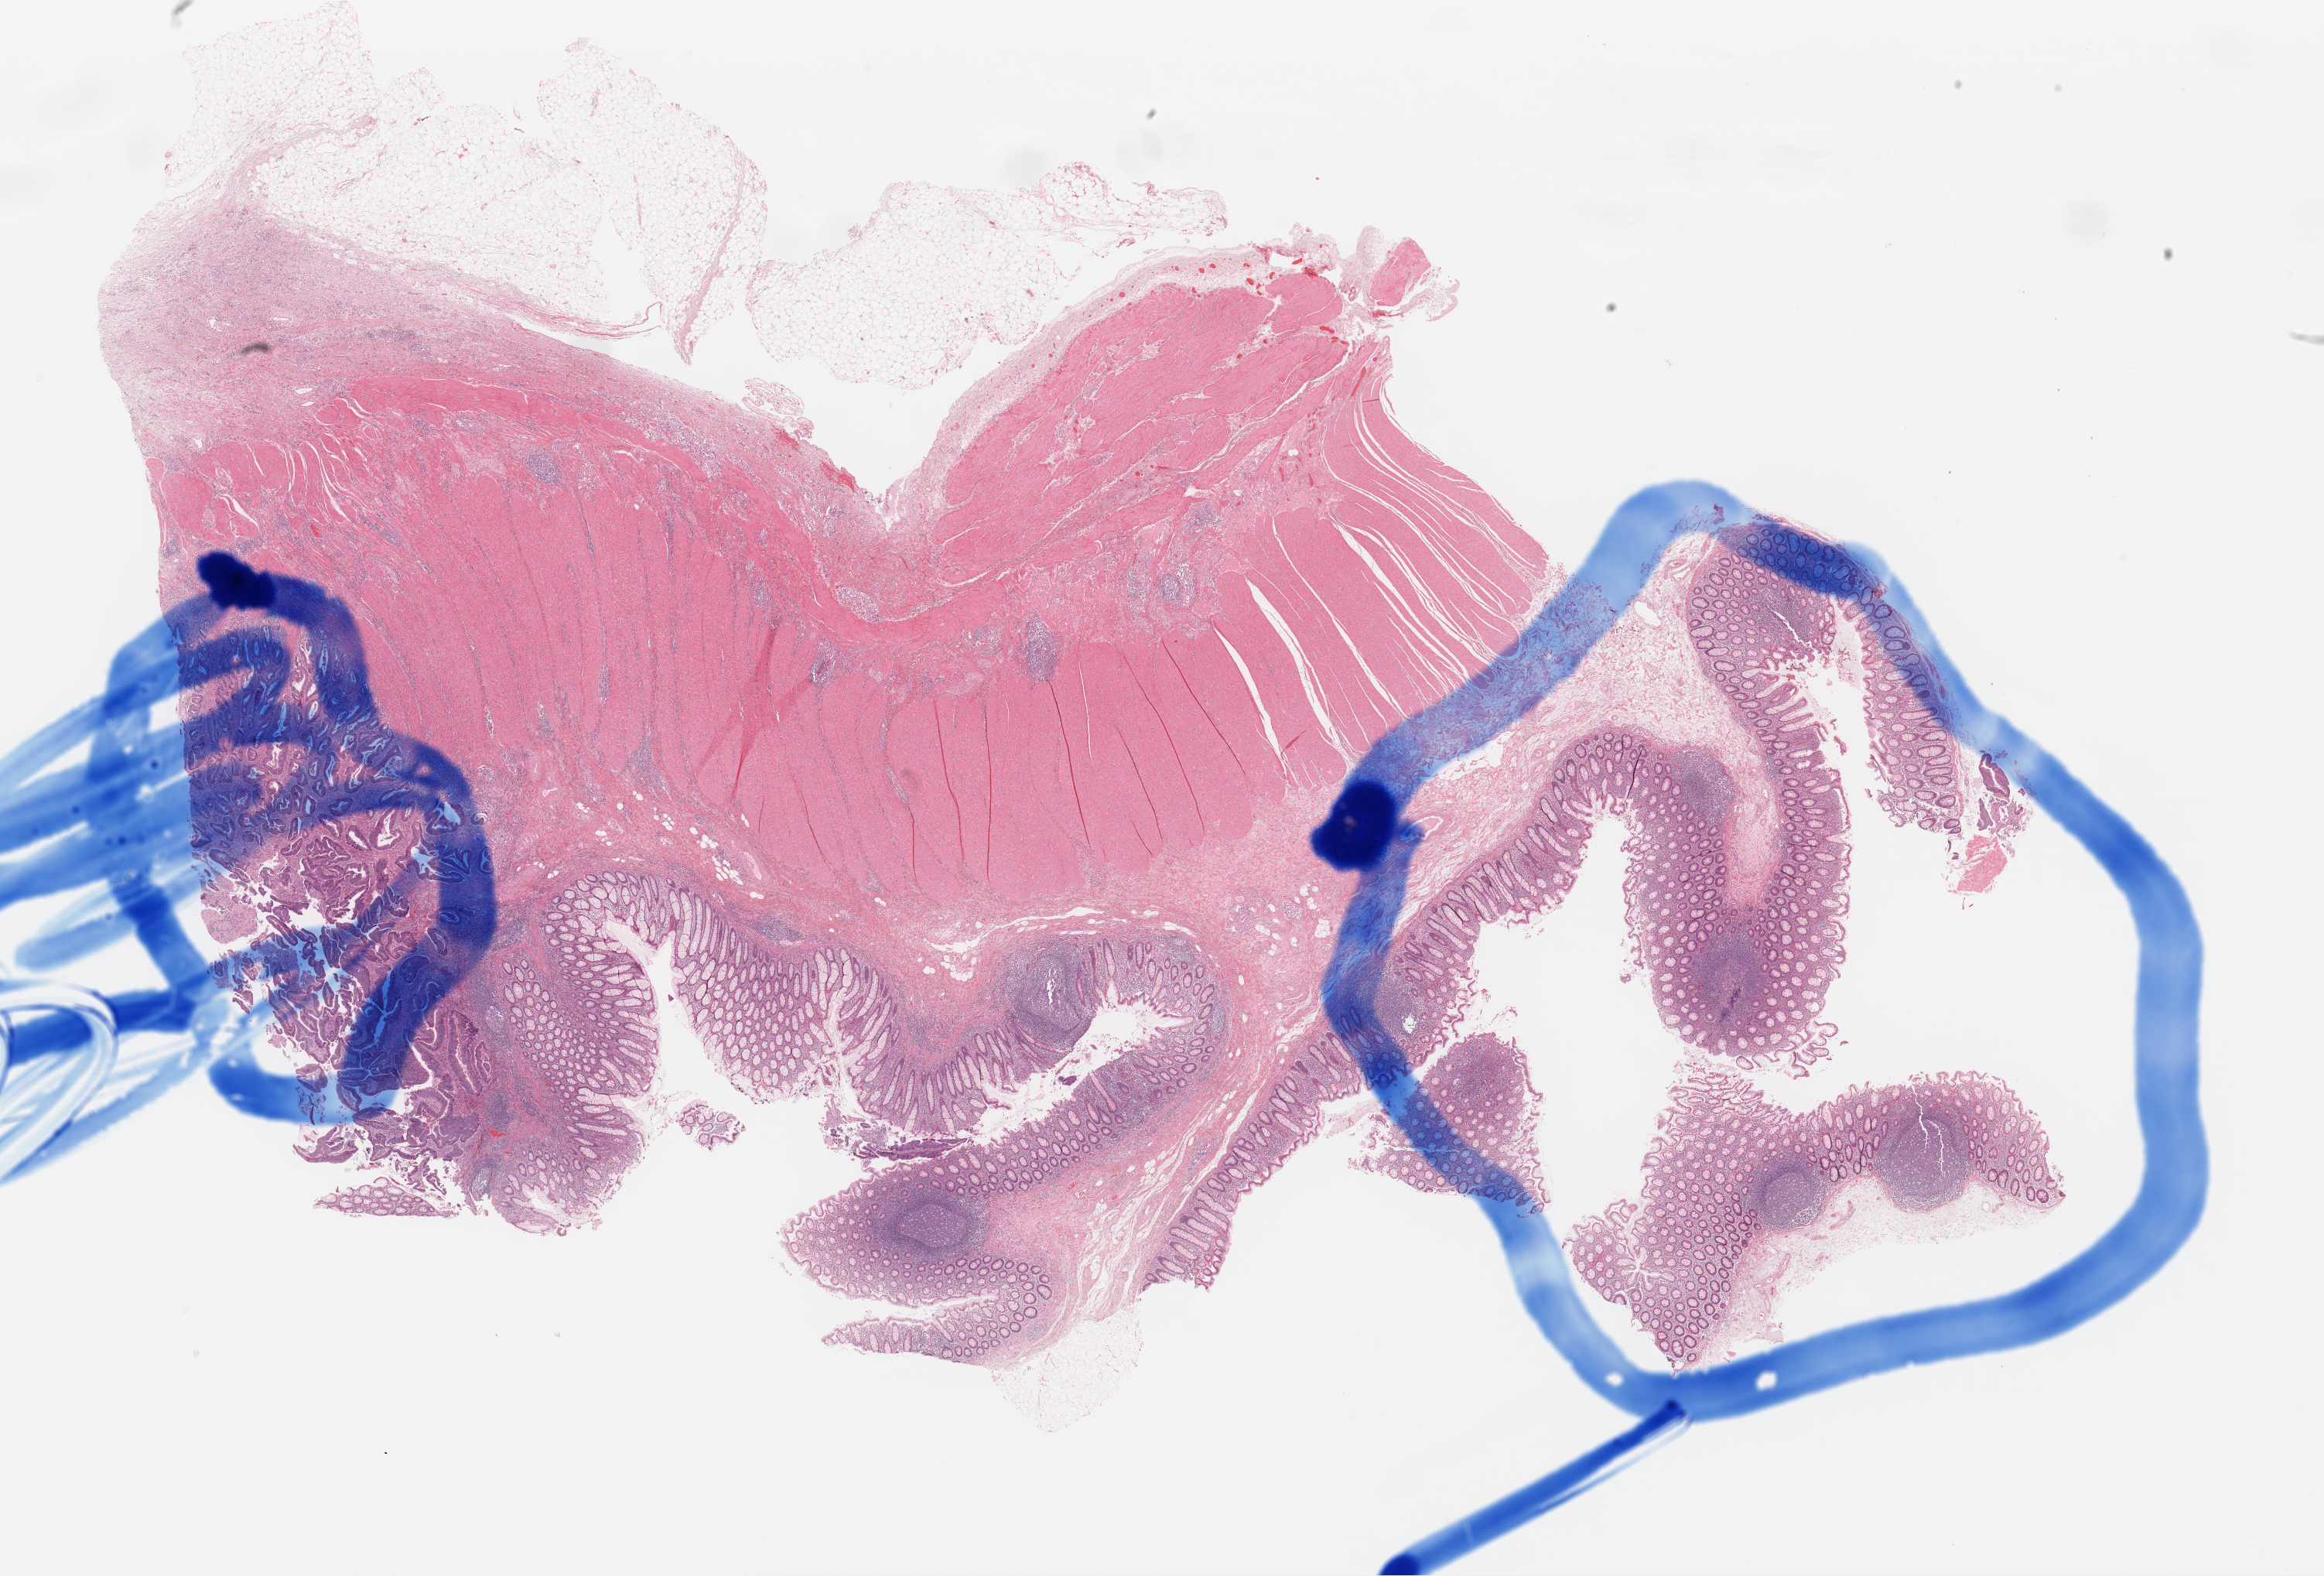
Whole-slide histology image, H&E-stained — whole scanned area (about 23.7 x 16.1 mm) shown as a low-resolution overview, formalin-fixed paraffin-embedded (FFPE) diagnostic section, sample: primary tumour, colon. Patient: male, age at initial diagnosis 73 years.
• diagnosis: Adenocarcinoma, NOS (sigmoid colon)
• AJCC pathologic stage: IIIB (6th edition)
• lymph nodes positive (case pathology): 1 of 23 examined